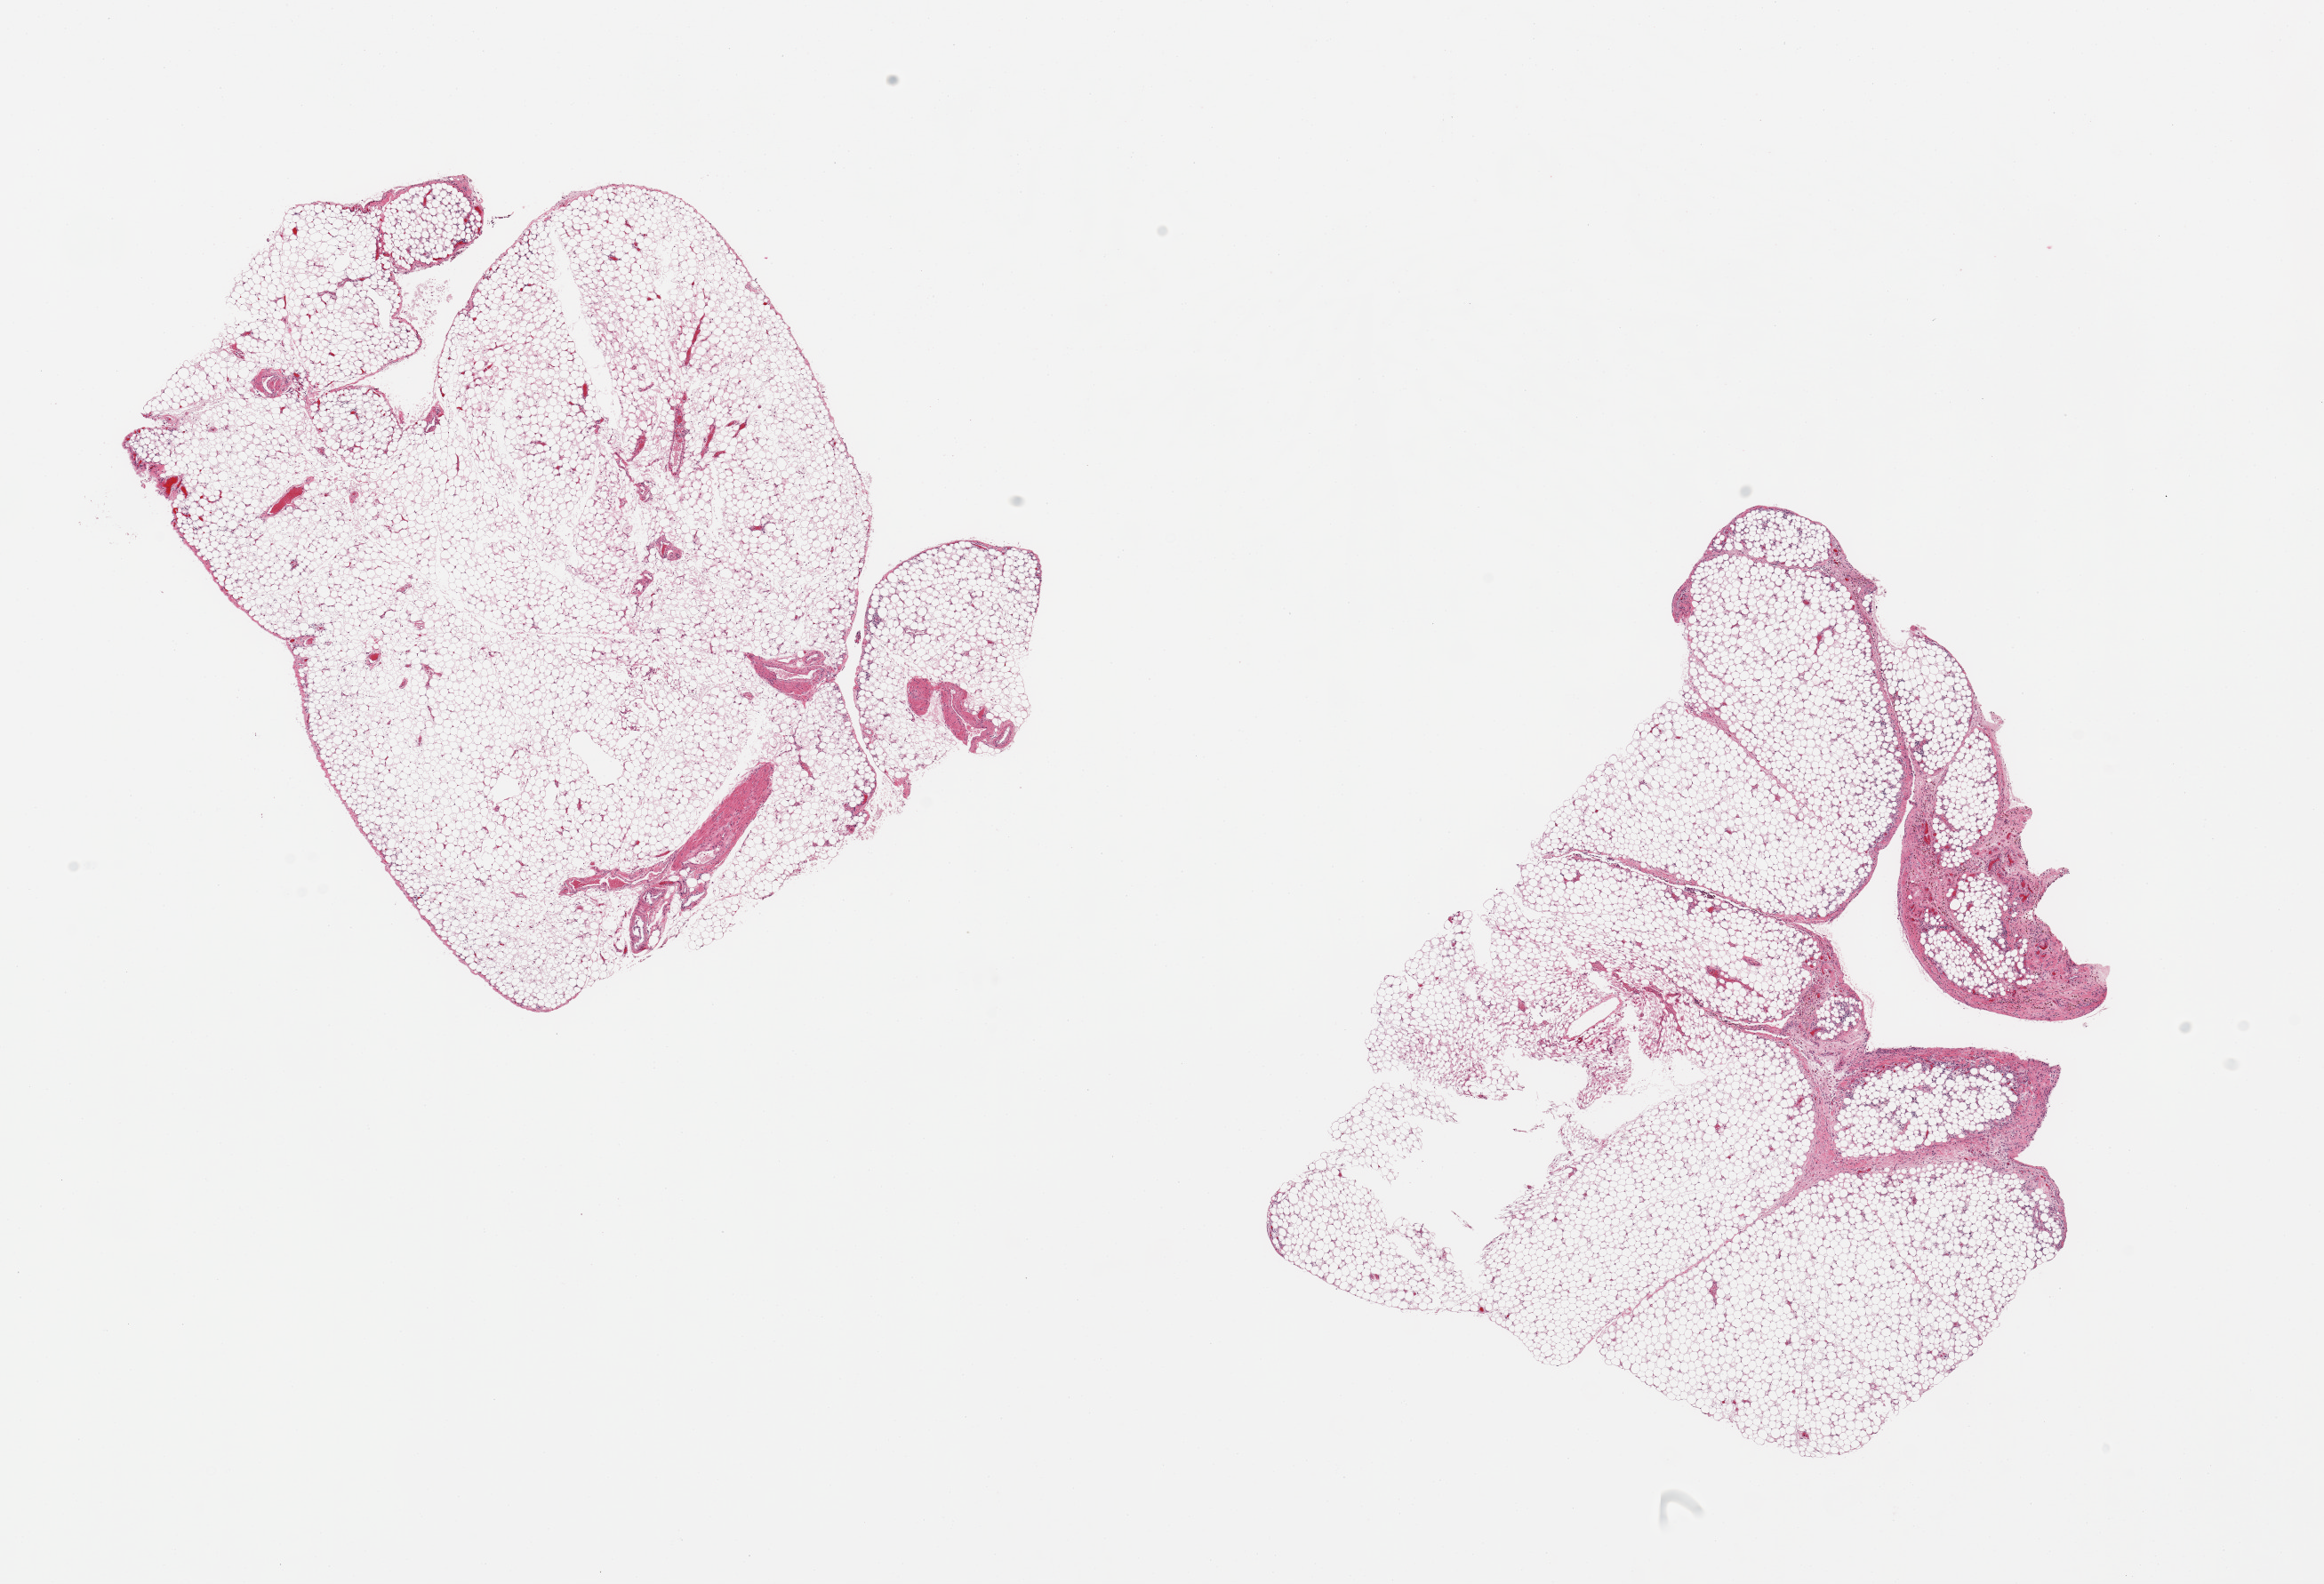
Whole-slide image, H&E stain — low-resolution overview of the scanned area, about 20.7 x 14.1 mm (acquisition: 20x scan); PAXgene-fixed paraffin-embedded (PFPE) section; section of omentum (target tissue); tissue donor sample.
Pathologist's review note for this sample: 2 pieces; predominantly fat with ~10% fibrovascular tissue with inflammatory cells and hemosiderin-laden macrophages.